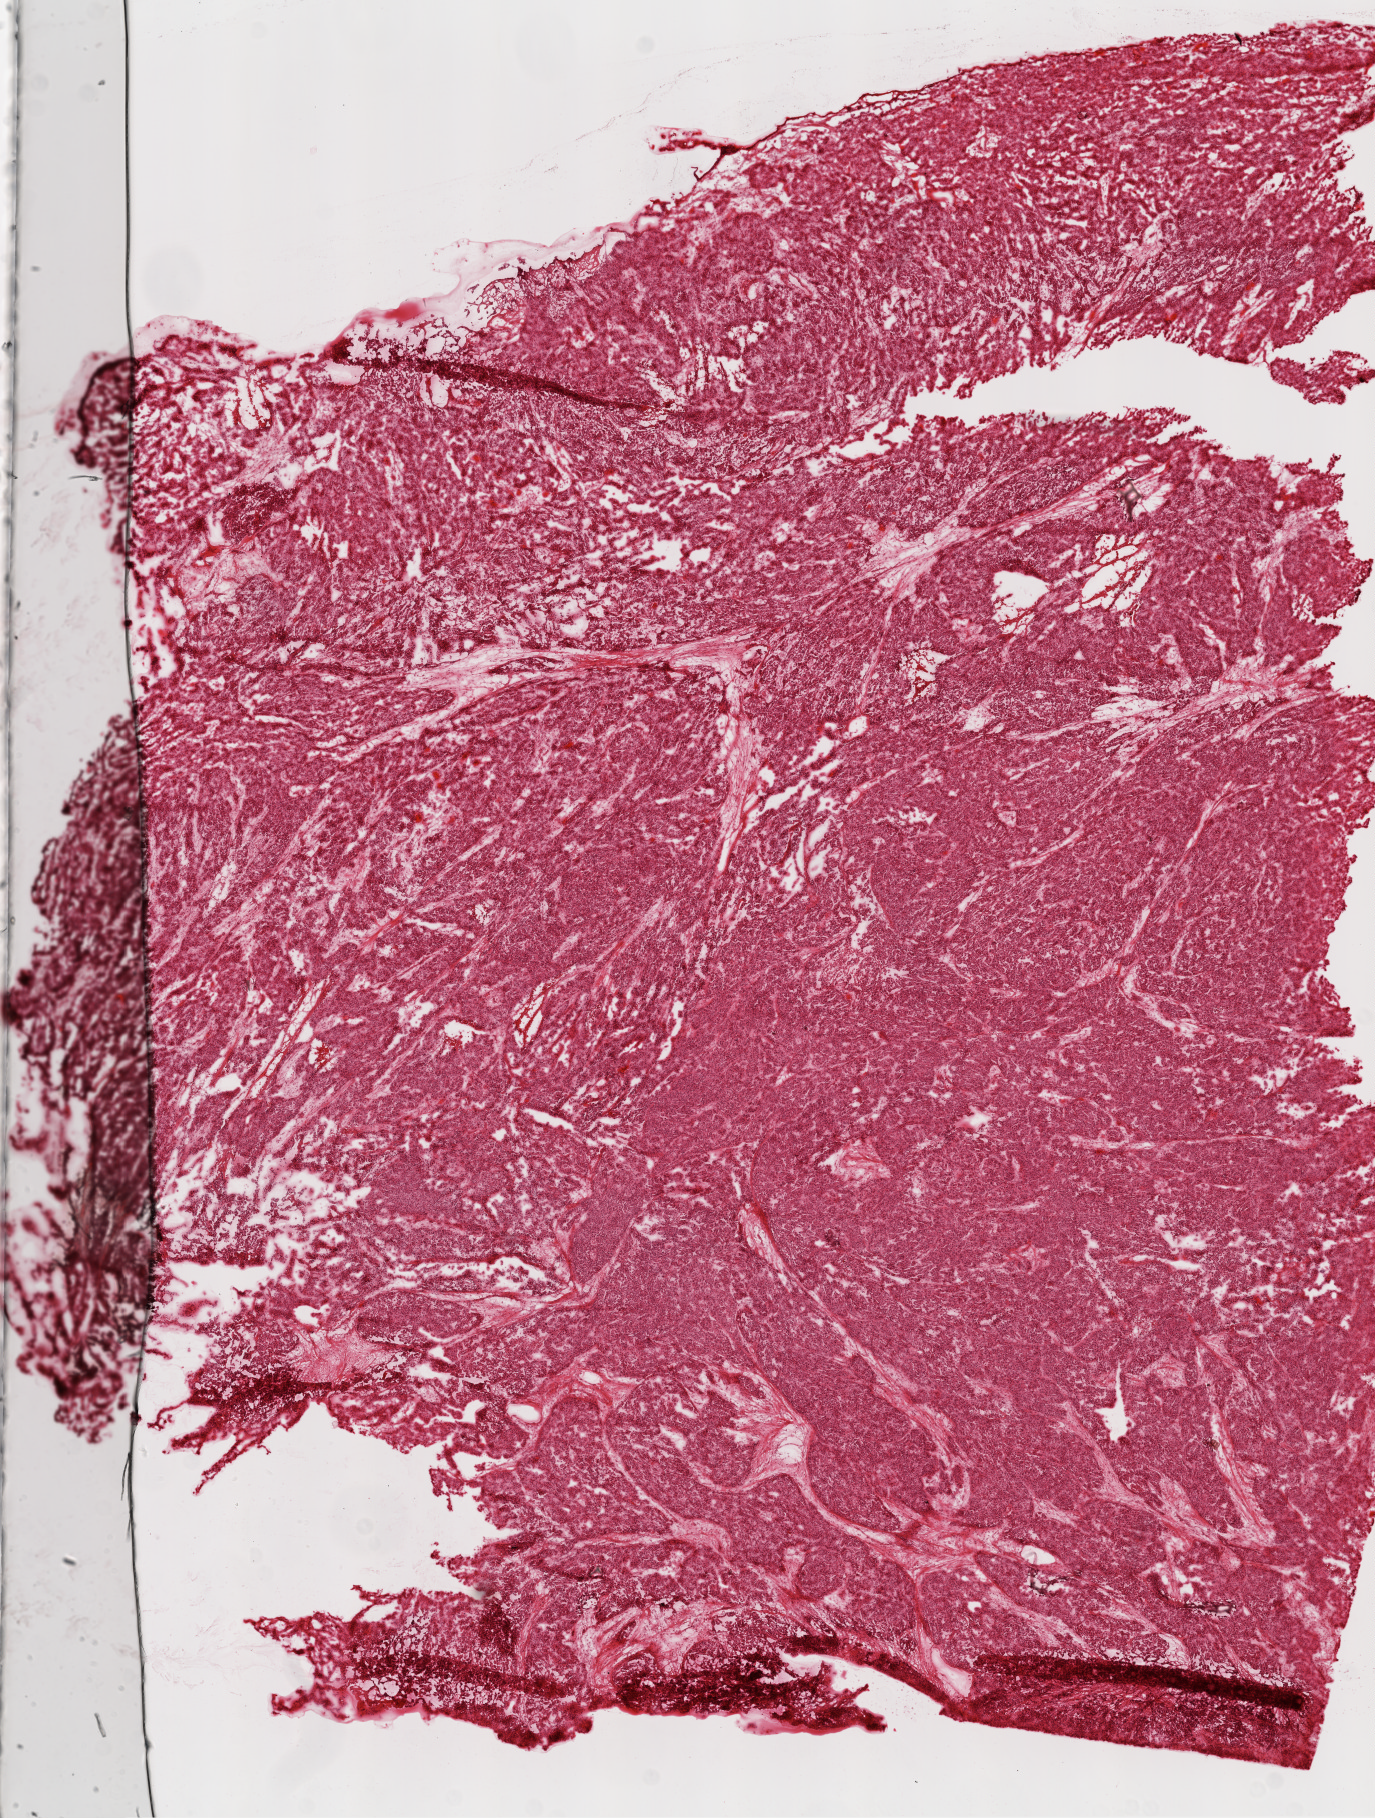
Hematoxylin and eosin (H&E) stained whole-slide image, low-resolution overview of the scanned area, about 11.0 x 14.6 mm, frozen section from the top of the tissue portion, ovary, primary tumour sample. Female, age 73 years at initial diagnosis. Histologic grade: G3 (poorly differentiated). Slide review estimates, as recorded: tumour cells 98%, tumour nuclei 95%, normal cells 0%, stromal cells 2%, necrosis 0%.
FIGO stage: IIIC. Histologic diagnosis: Serous cystadenocarcinoma, NOS.